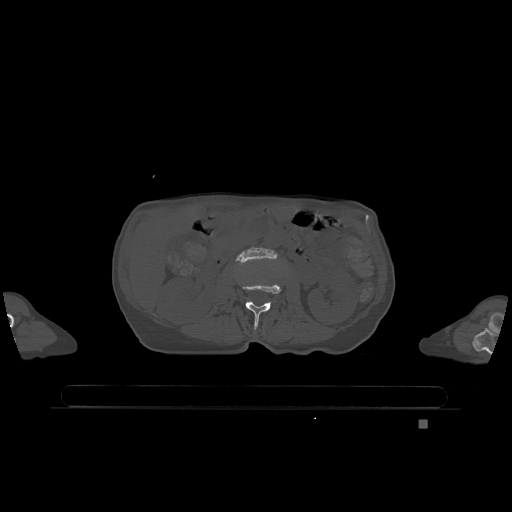
CT including the spine, one axial slice; slice 401 of 1317 in the series (ordered by position); bone window (W 1800 / L 400 HU); 0.5 mm slice thickness; 512 × 512 image matrix, field of view 500 × 500 mm. Female patient, age 74 years. Case-level facts recorded for this patient, not image findings: primary cancer: lung; vertebrae with lytic lesions (as recorded): T1, T4, T5, T6, L4, L5.
Structures marked on this image (semi-automatic segmentation, software-assisted and operator-edited):
- L2 vertebra: bounding box [x1, y1, x2, y2] px = [242, 283, 282, 330]
- L3 vertebra: [236, 247, 277, 264]